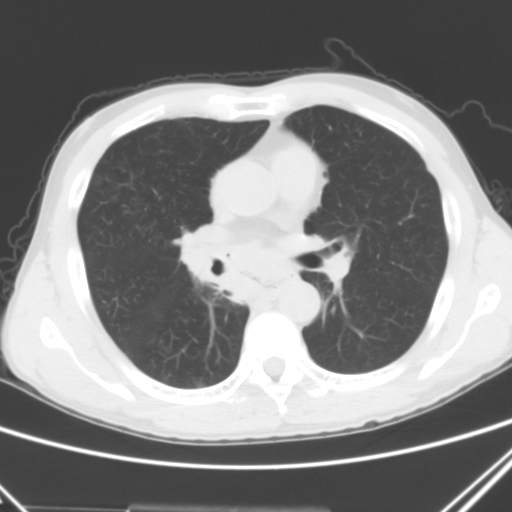
Chest CT, one axial slice; position 26 of 51 along the scan axis; 120 kVp; lung window (W 1500 / L -600 HU); 5 mm slice thickness; 512 × 512 image matrix, field of view 327 × 327 mm. Male patient, age 52 years. From the clinical record (not read from this slice): clinical TNM (as recorded): T2a N0 M1c.
Annotated regions visible in this slice (rectangle marked by the reading radiologist):
- lung tumour (recorded histology: squamous cell carcinoma): bounding box [x1, y1, x2, y2] px = [175, 209, 245, 315]